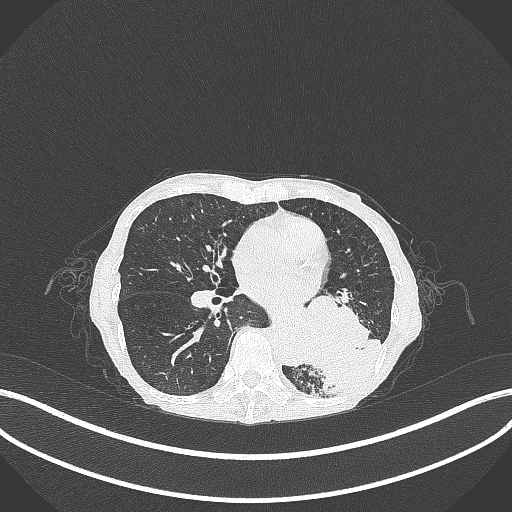
Chest CT, one axial slice. Slice 122 of 347 in the series (ordered by position). Reconstruction kernel B70f. Lung window (W 1500 / L -600 HU). 512 × 512 image matrix. Patient: female, 70 years. From the clinical record (not read from this slice): clinical TNM (as recorded): T3 N0 M0; histopathological grade: G3.
Structures marked on this image (rectangle marked by the reading radiologist):
- lung tumour (recorded histology: small cell carcinoma): bounding box [x1, y1, x2, y2] px = [288, 289, 384, 395]